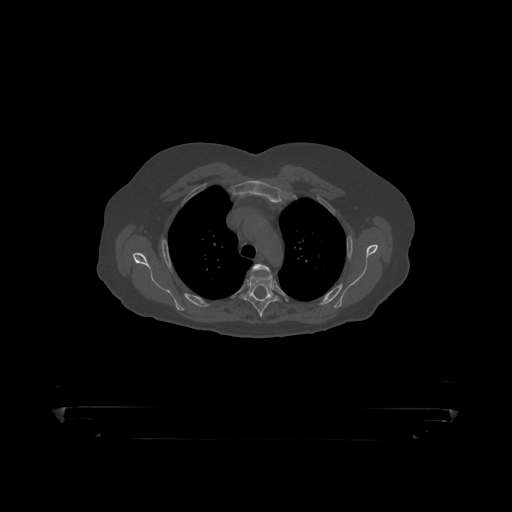
CT including the spine, one axial slice; position 341 of 390 along the scan axis; reconstruction kernel STANDARD; 120 kVp; bone window (W 1800 / L 400 HU); 1.25 mm slice thickness; 512 × 512 image matrix, field of view 650 × 650 mm. Patient: male, 60 years. From the clinical record (not read from this slice): primary cancer: prostate.
Outlined on this slice (semi-automatically segmented with operator editing):
- T3 vertebra: bounding box (x1, y1, x2, y2) in pixels: (252, 264, 271, 273)
- T4 vertebra: (244, 264, 283, 319)